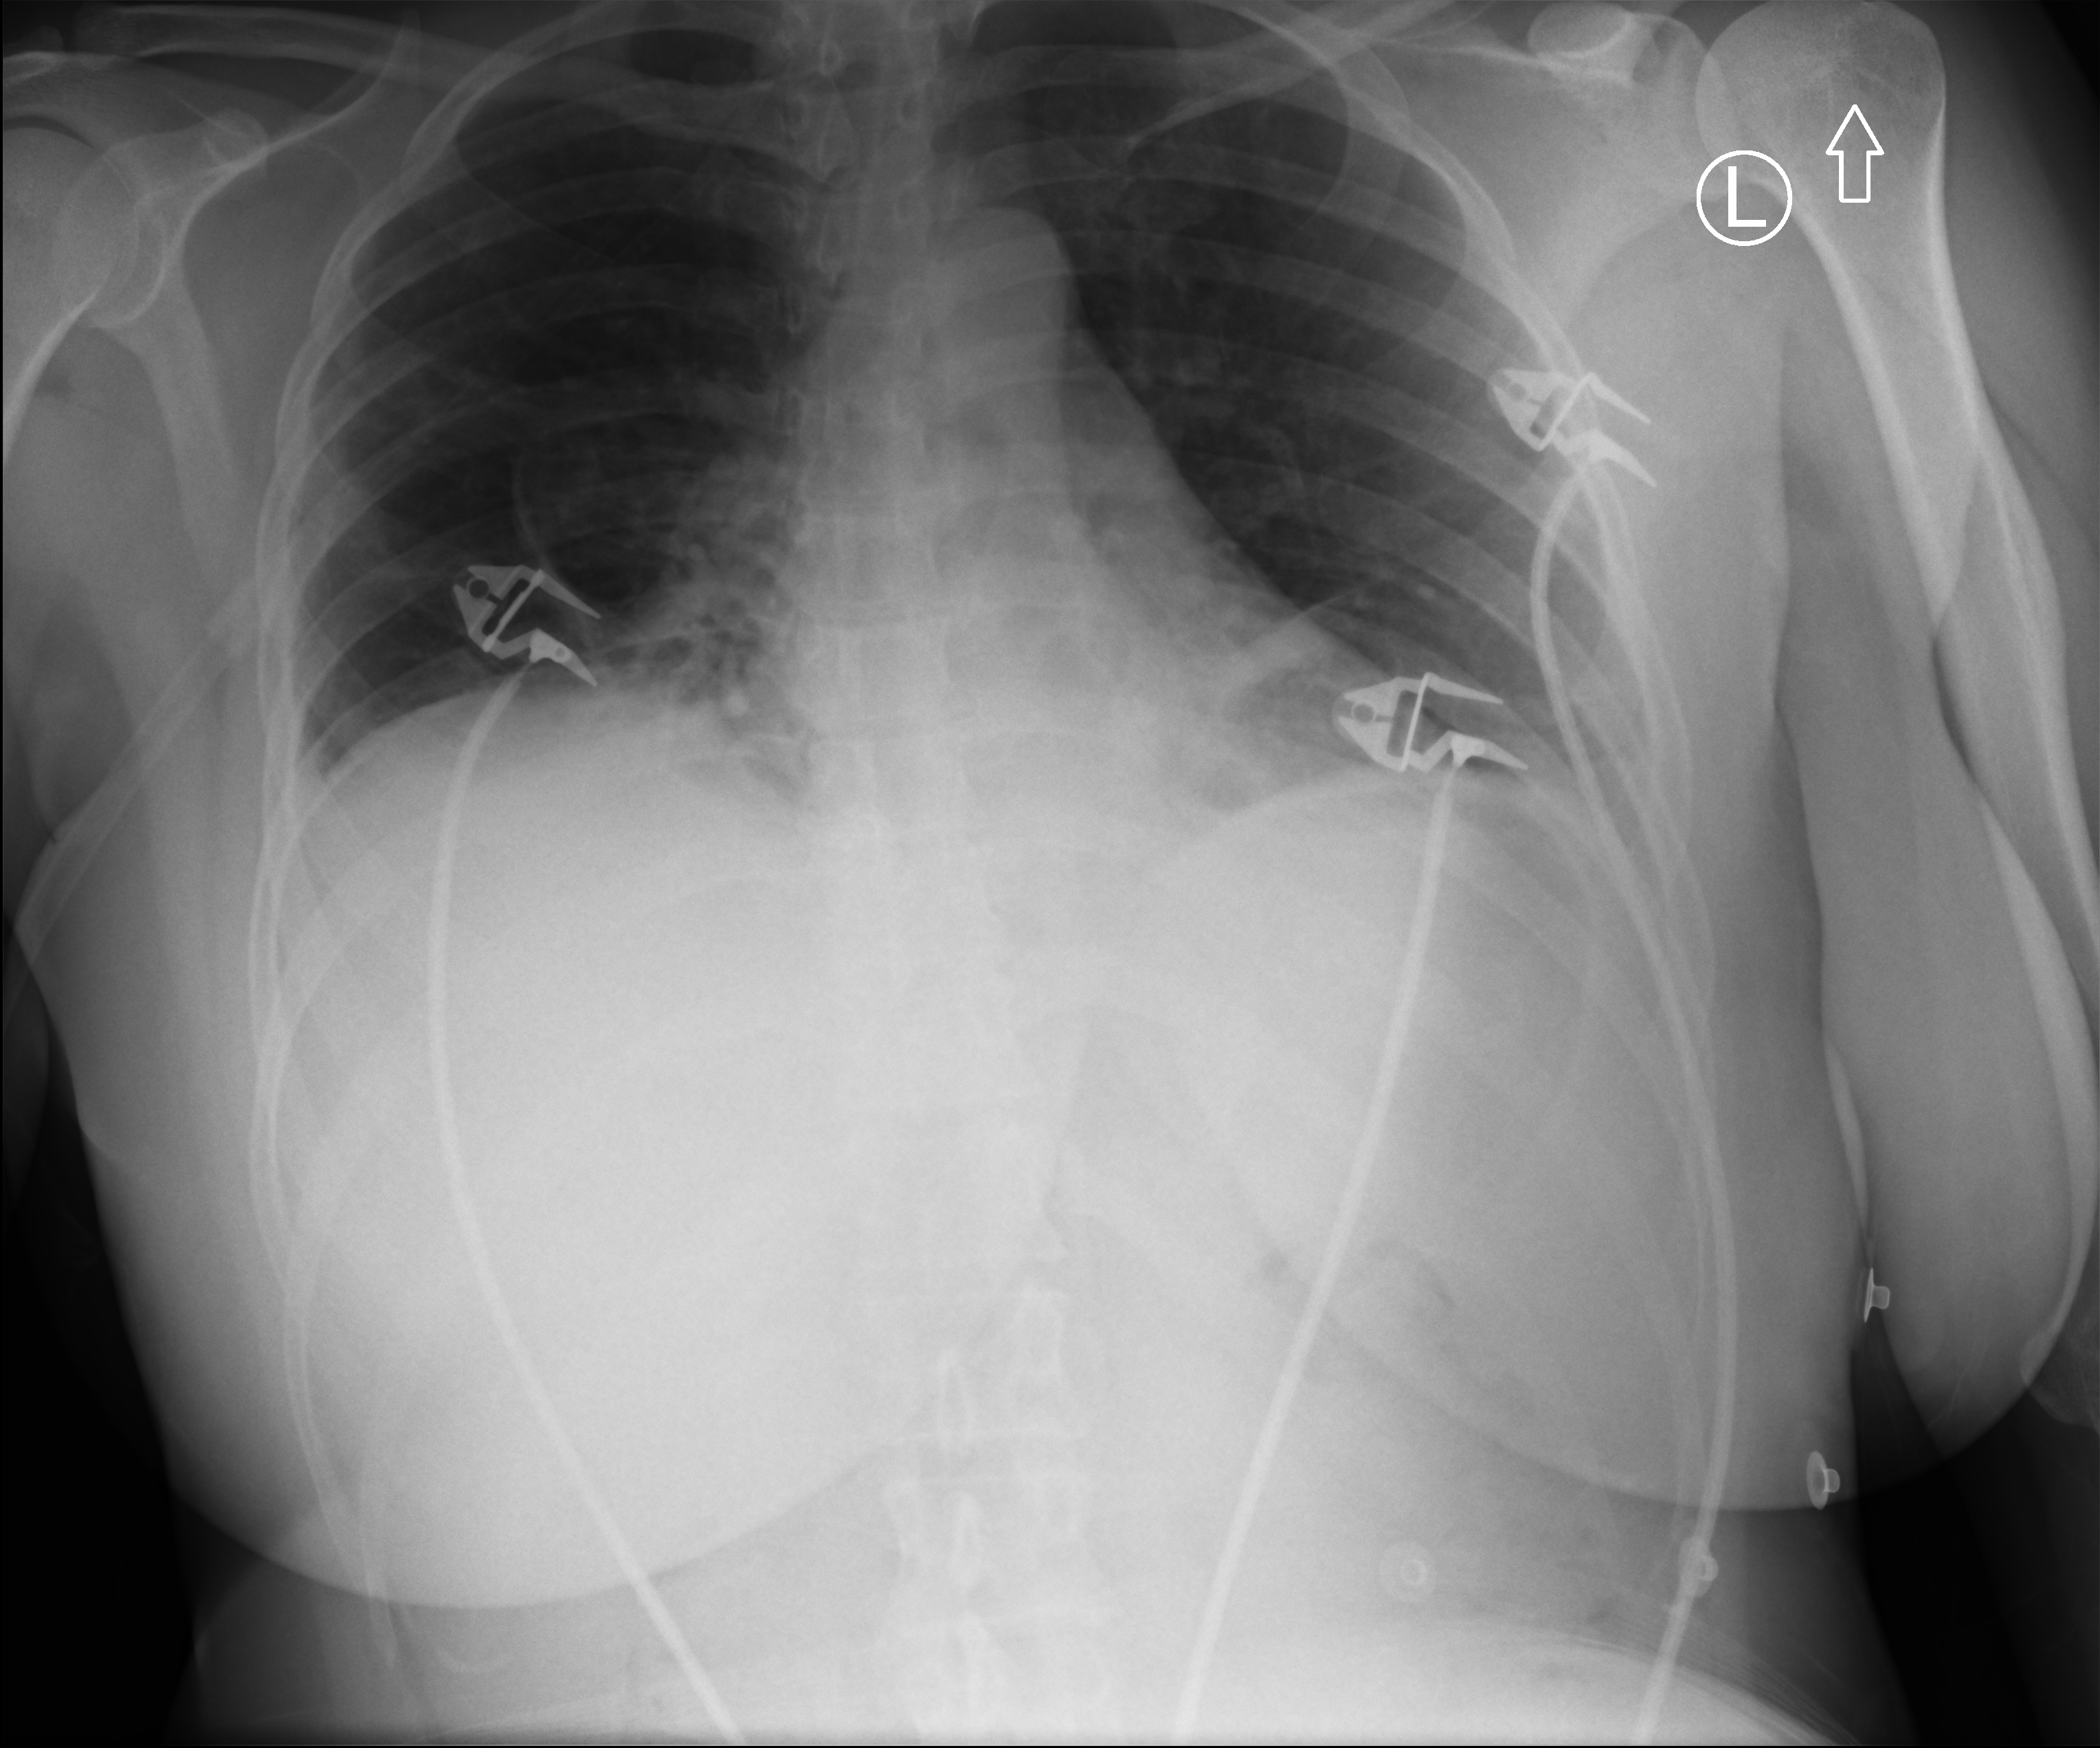
Bedside chest radiograph (computed radiography). Female patient hospitalised with COVID-19, age 18–59 years.
Admission-level facts for this patient (not findings on this image; timing relative to this image not recorded): length of hospital stay: 9 days; other chronic lung disease (admission record): yes.